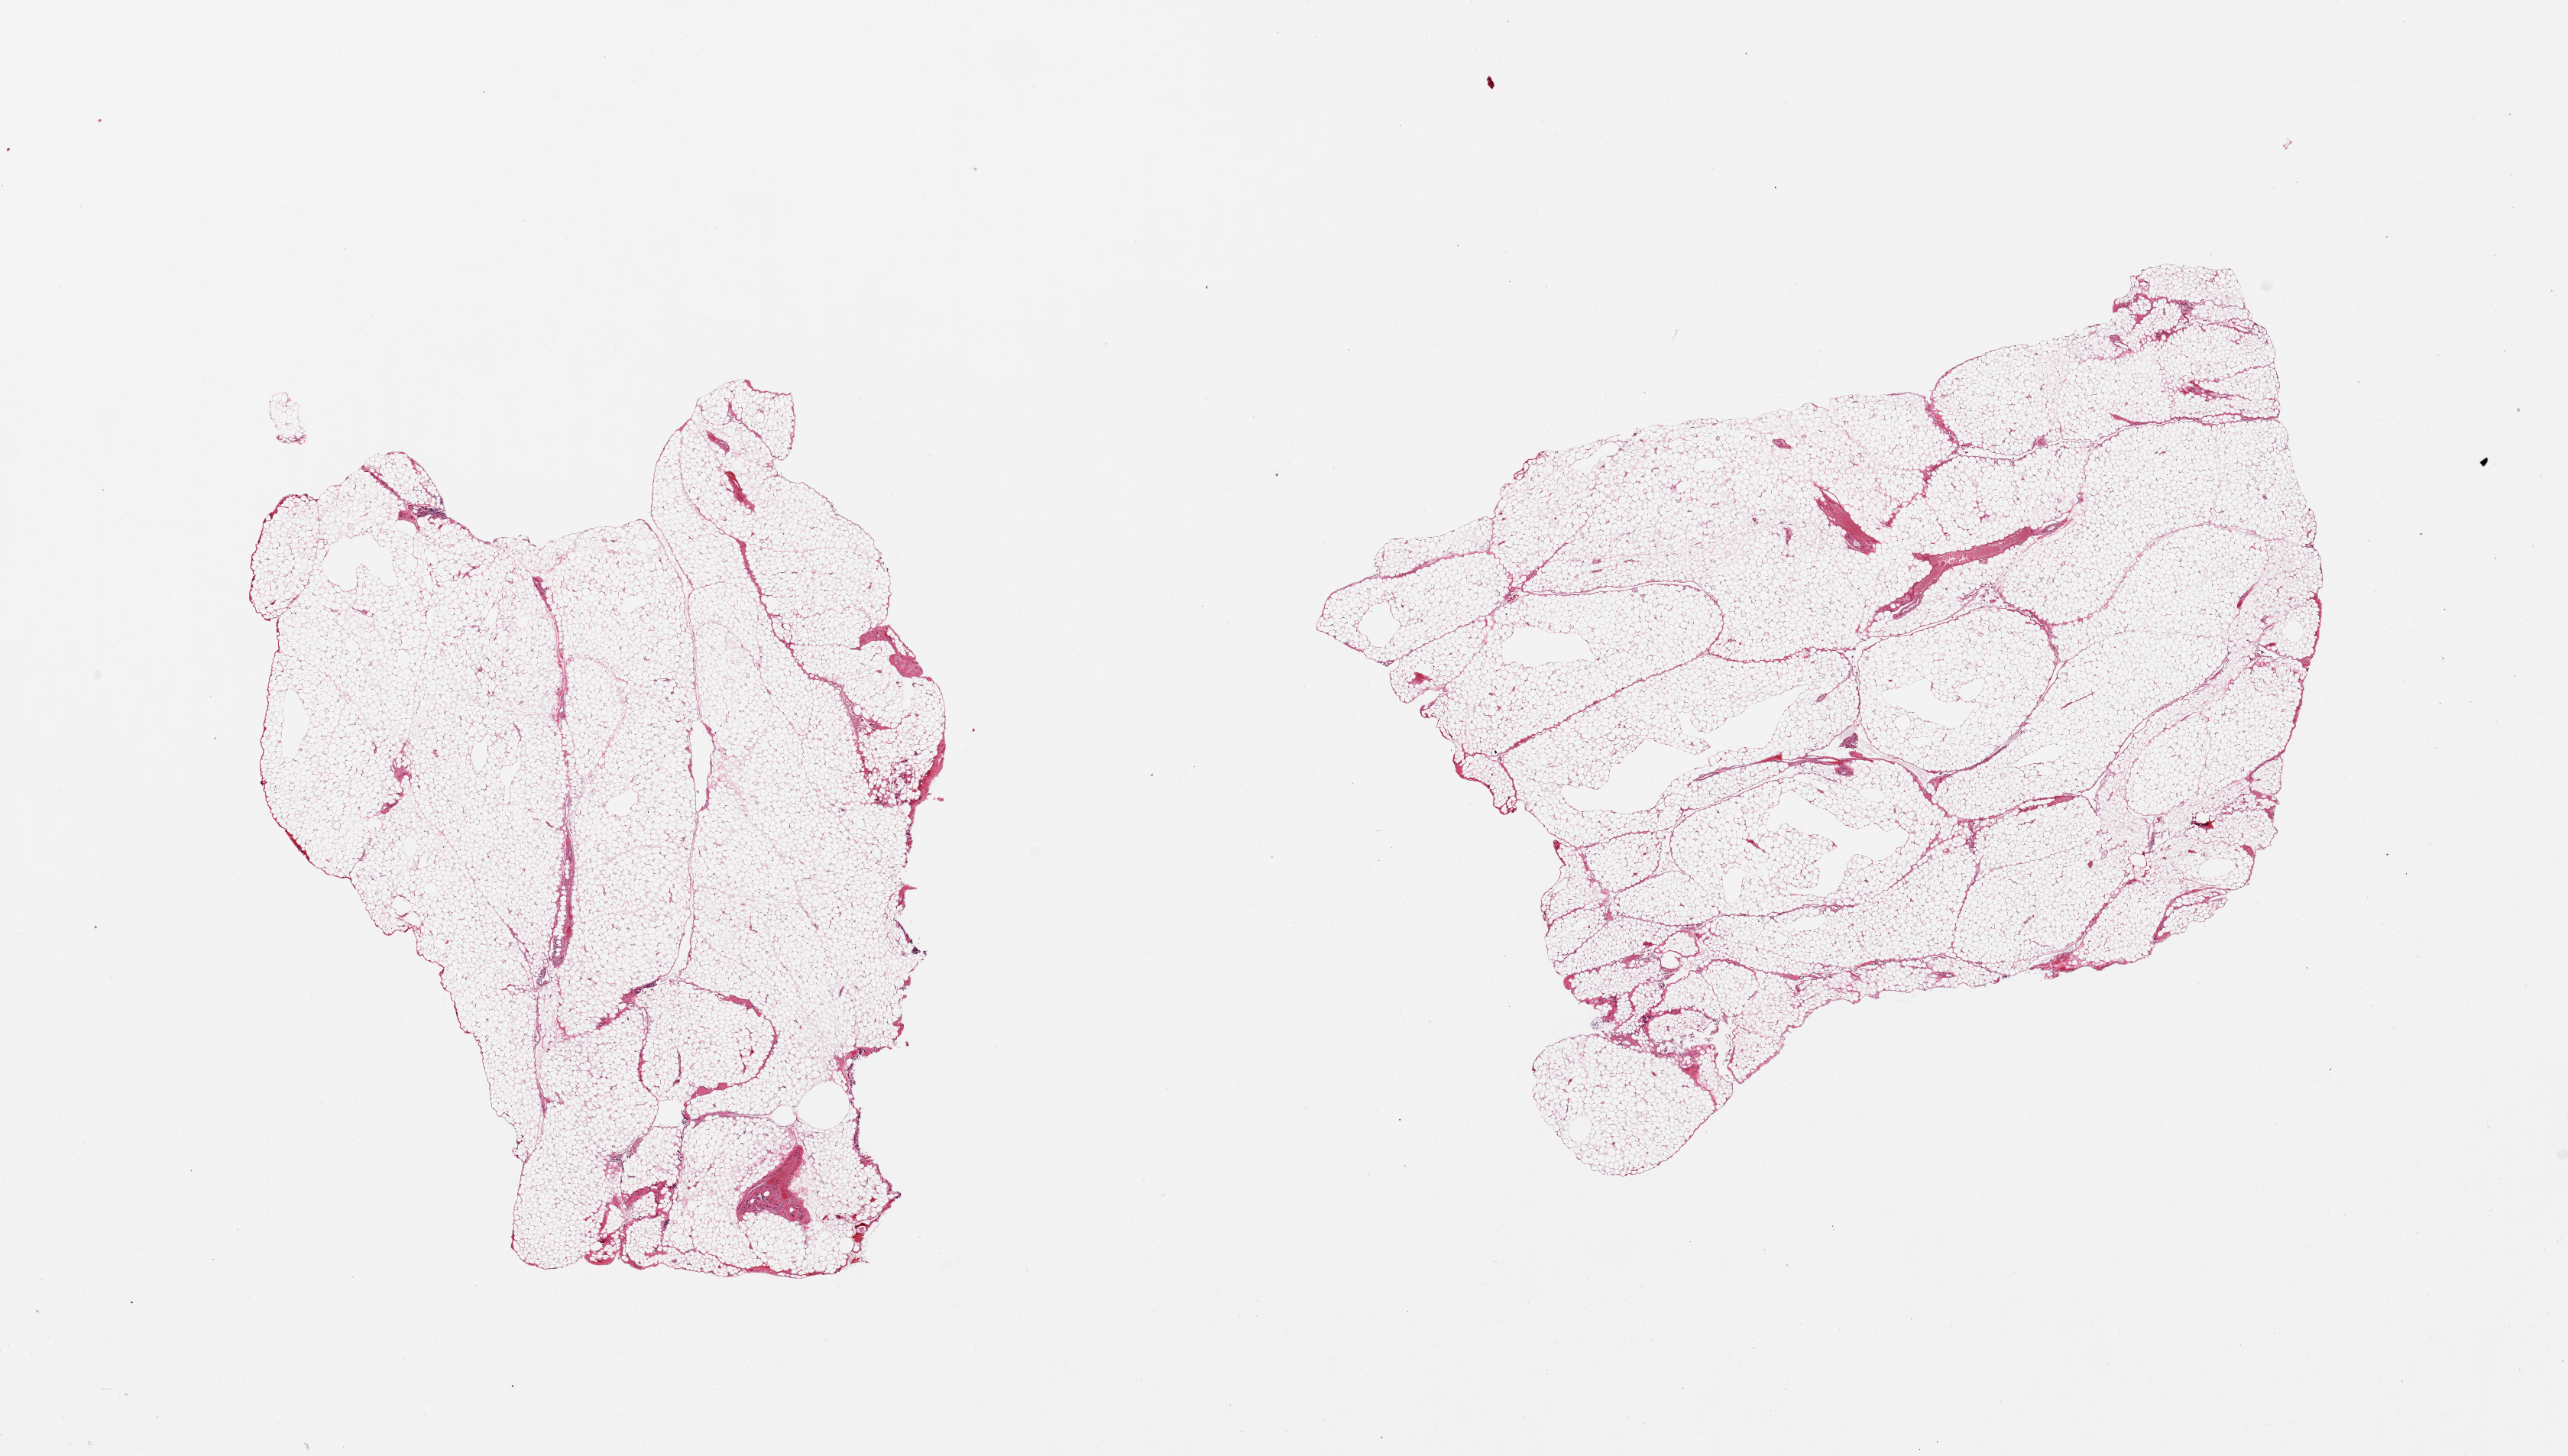
H&E whole-slide image — shown as a low-resolution overview of the whole scanned area (about 26.6 x 15.1 mm). PAXgene-fixed paraffin-embedded (PFPE) section. Target tissue: omentum. Donor tissue sample. Donor: male.
• reviewer comment on this tissue sample: 2 pieces